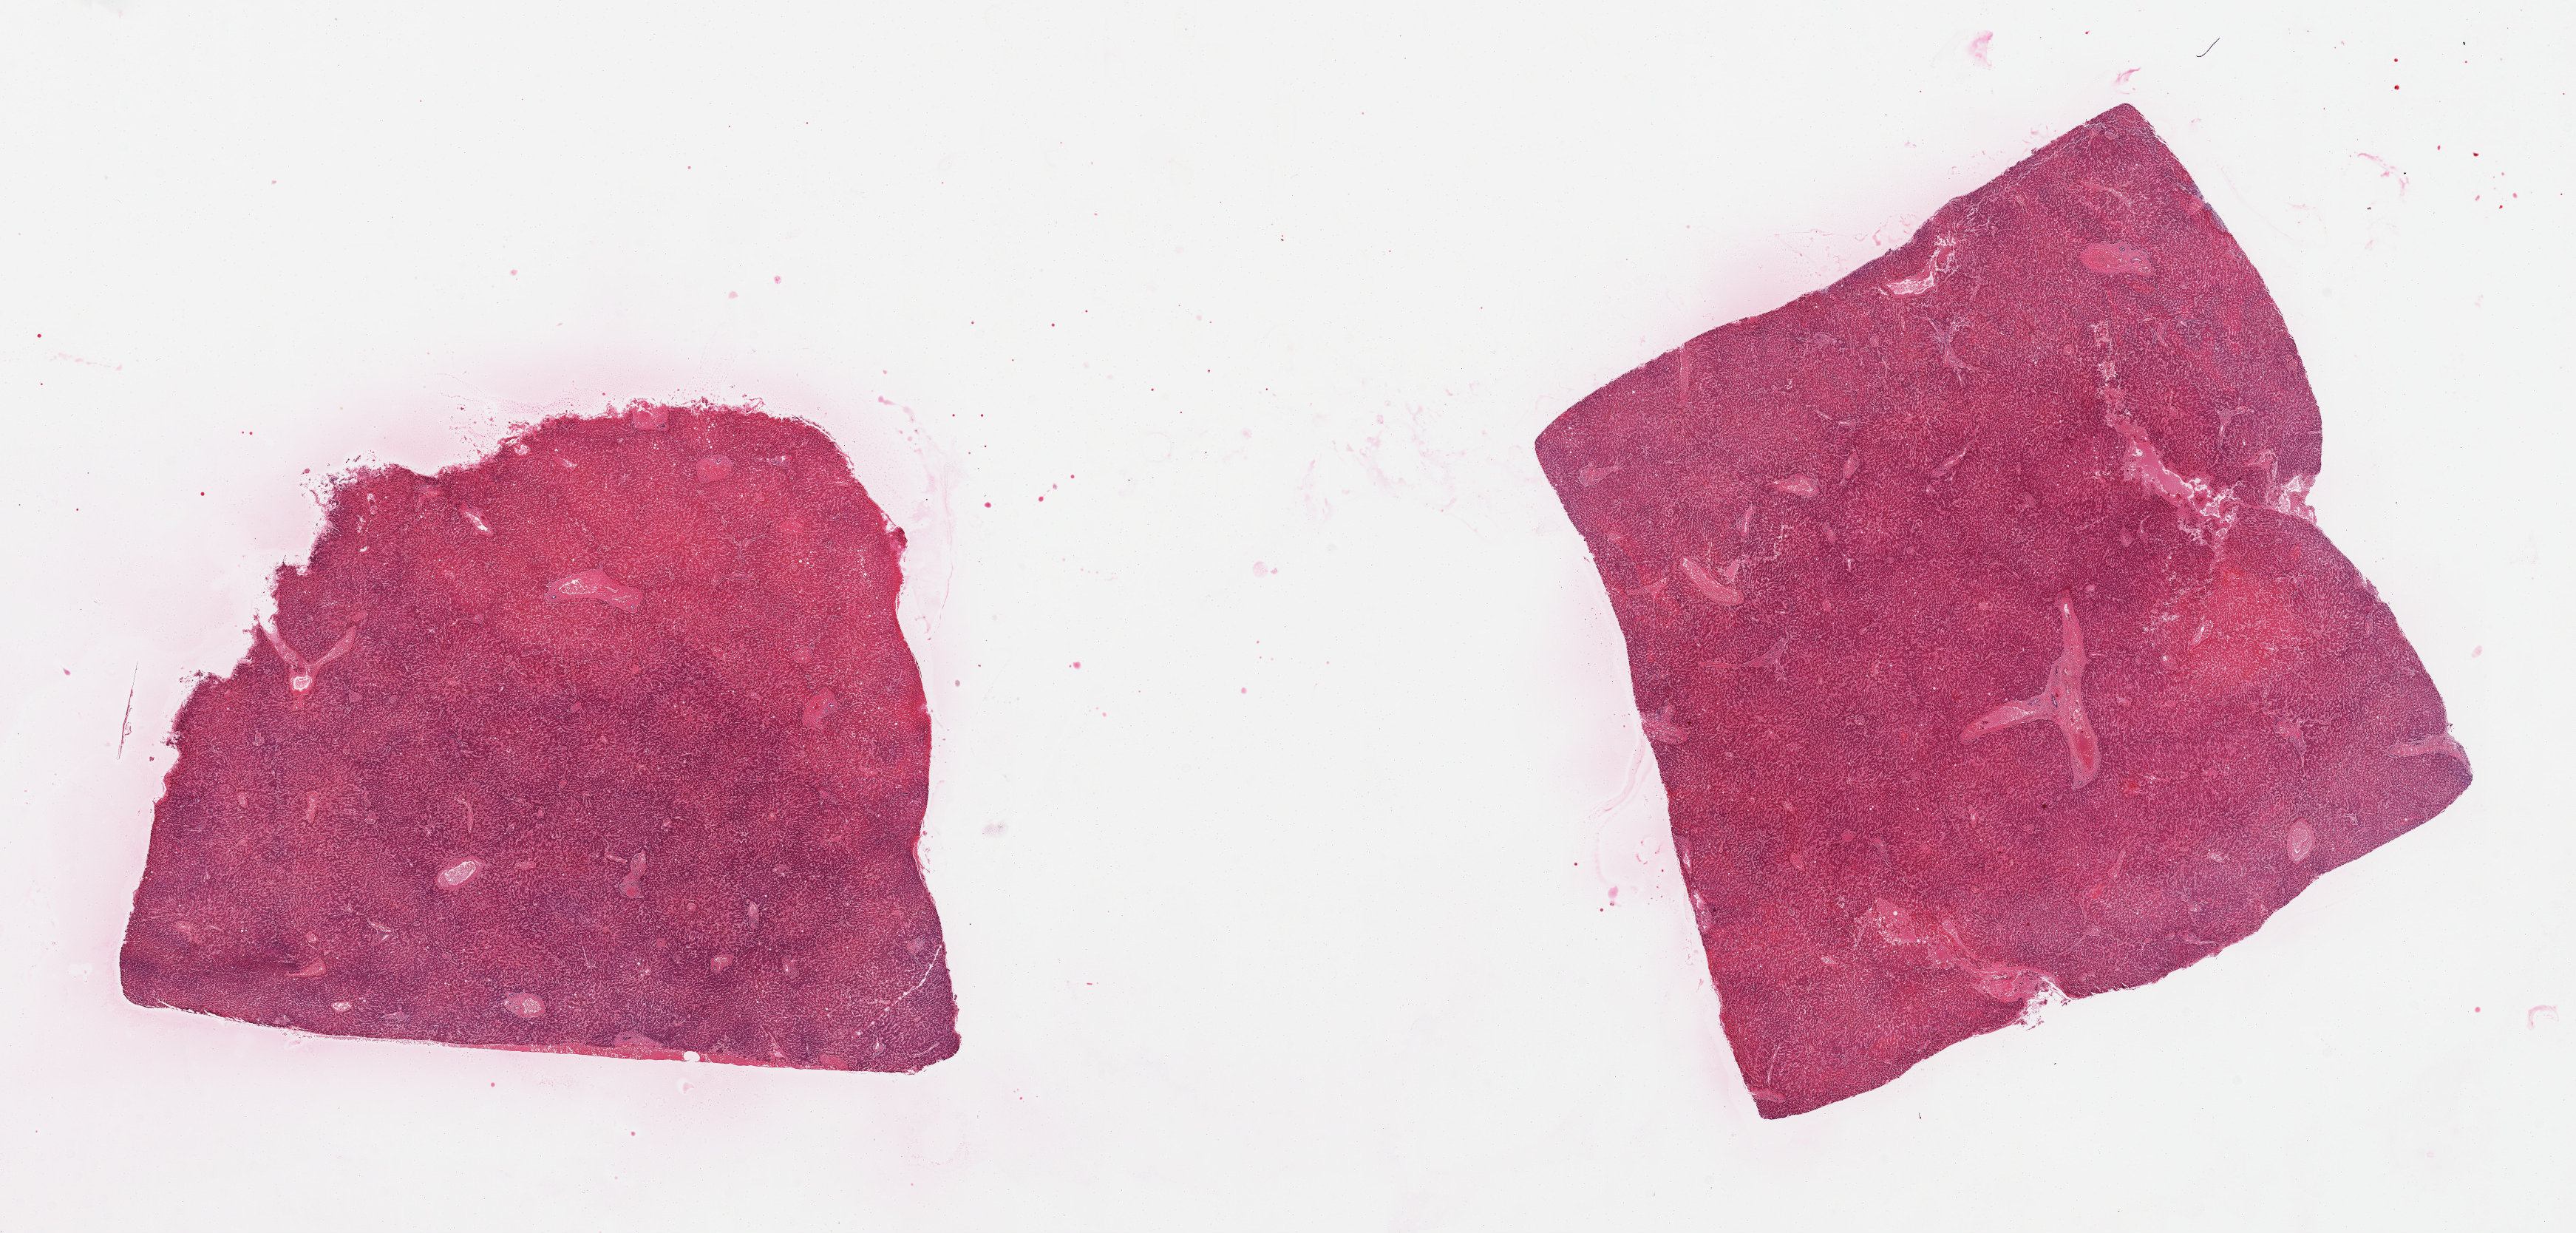
Haematoxylin and eosin whole-slide image, shown as a low-resolution overview of the whole scanned area (about 27.6 x 13.2 mm, slide scanned at 20x), PAXgene-fixed paraffin-embedded (PFPE) section, section of liver (target tissue), tissue donor sample. Donor sex: male.
Pathologist's review note for this sample: 2 pieces, congestion.